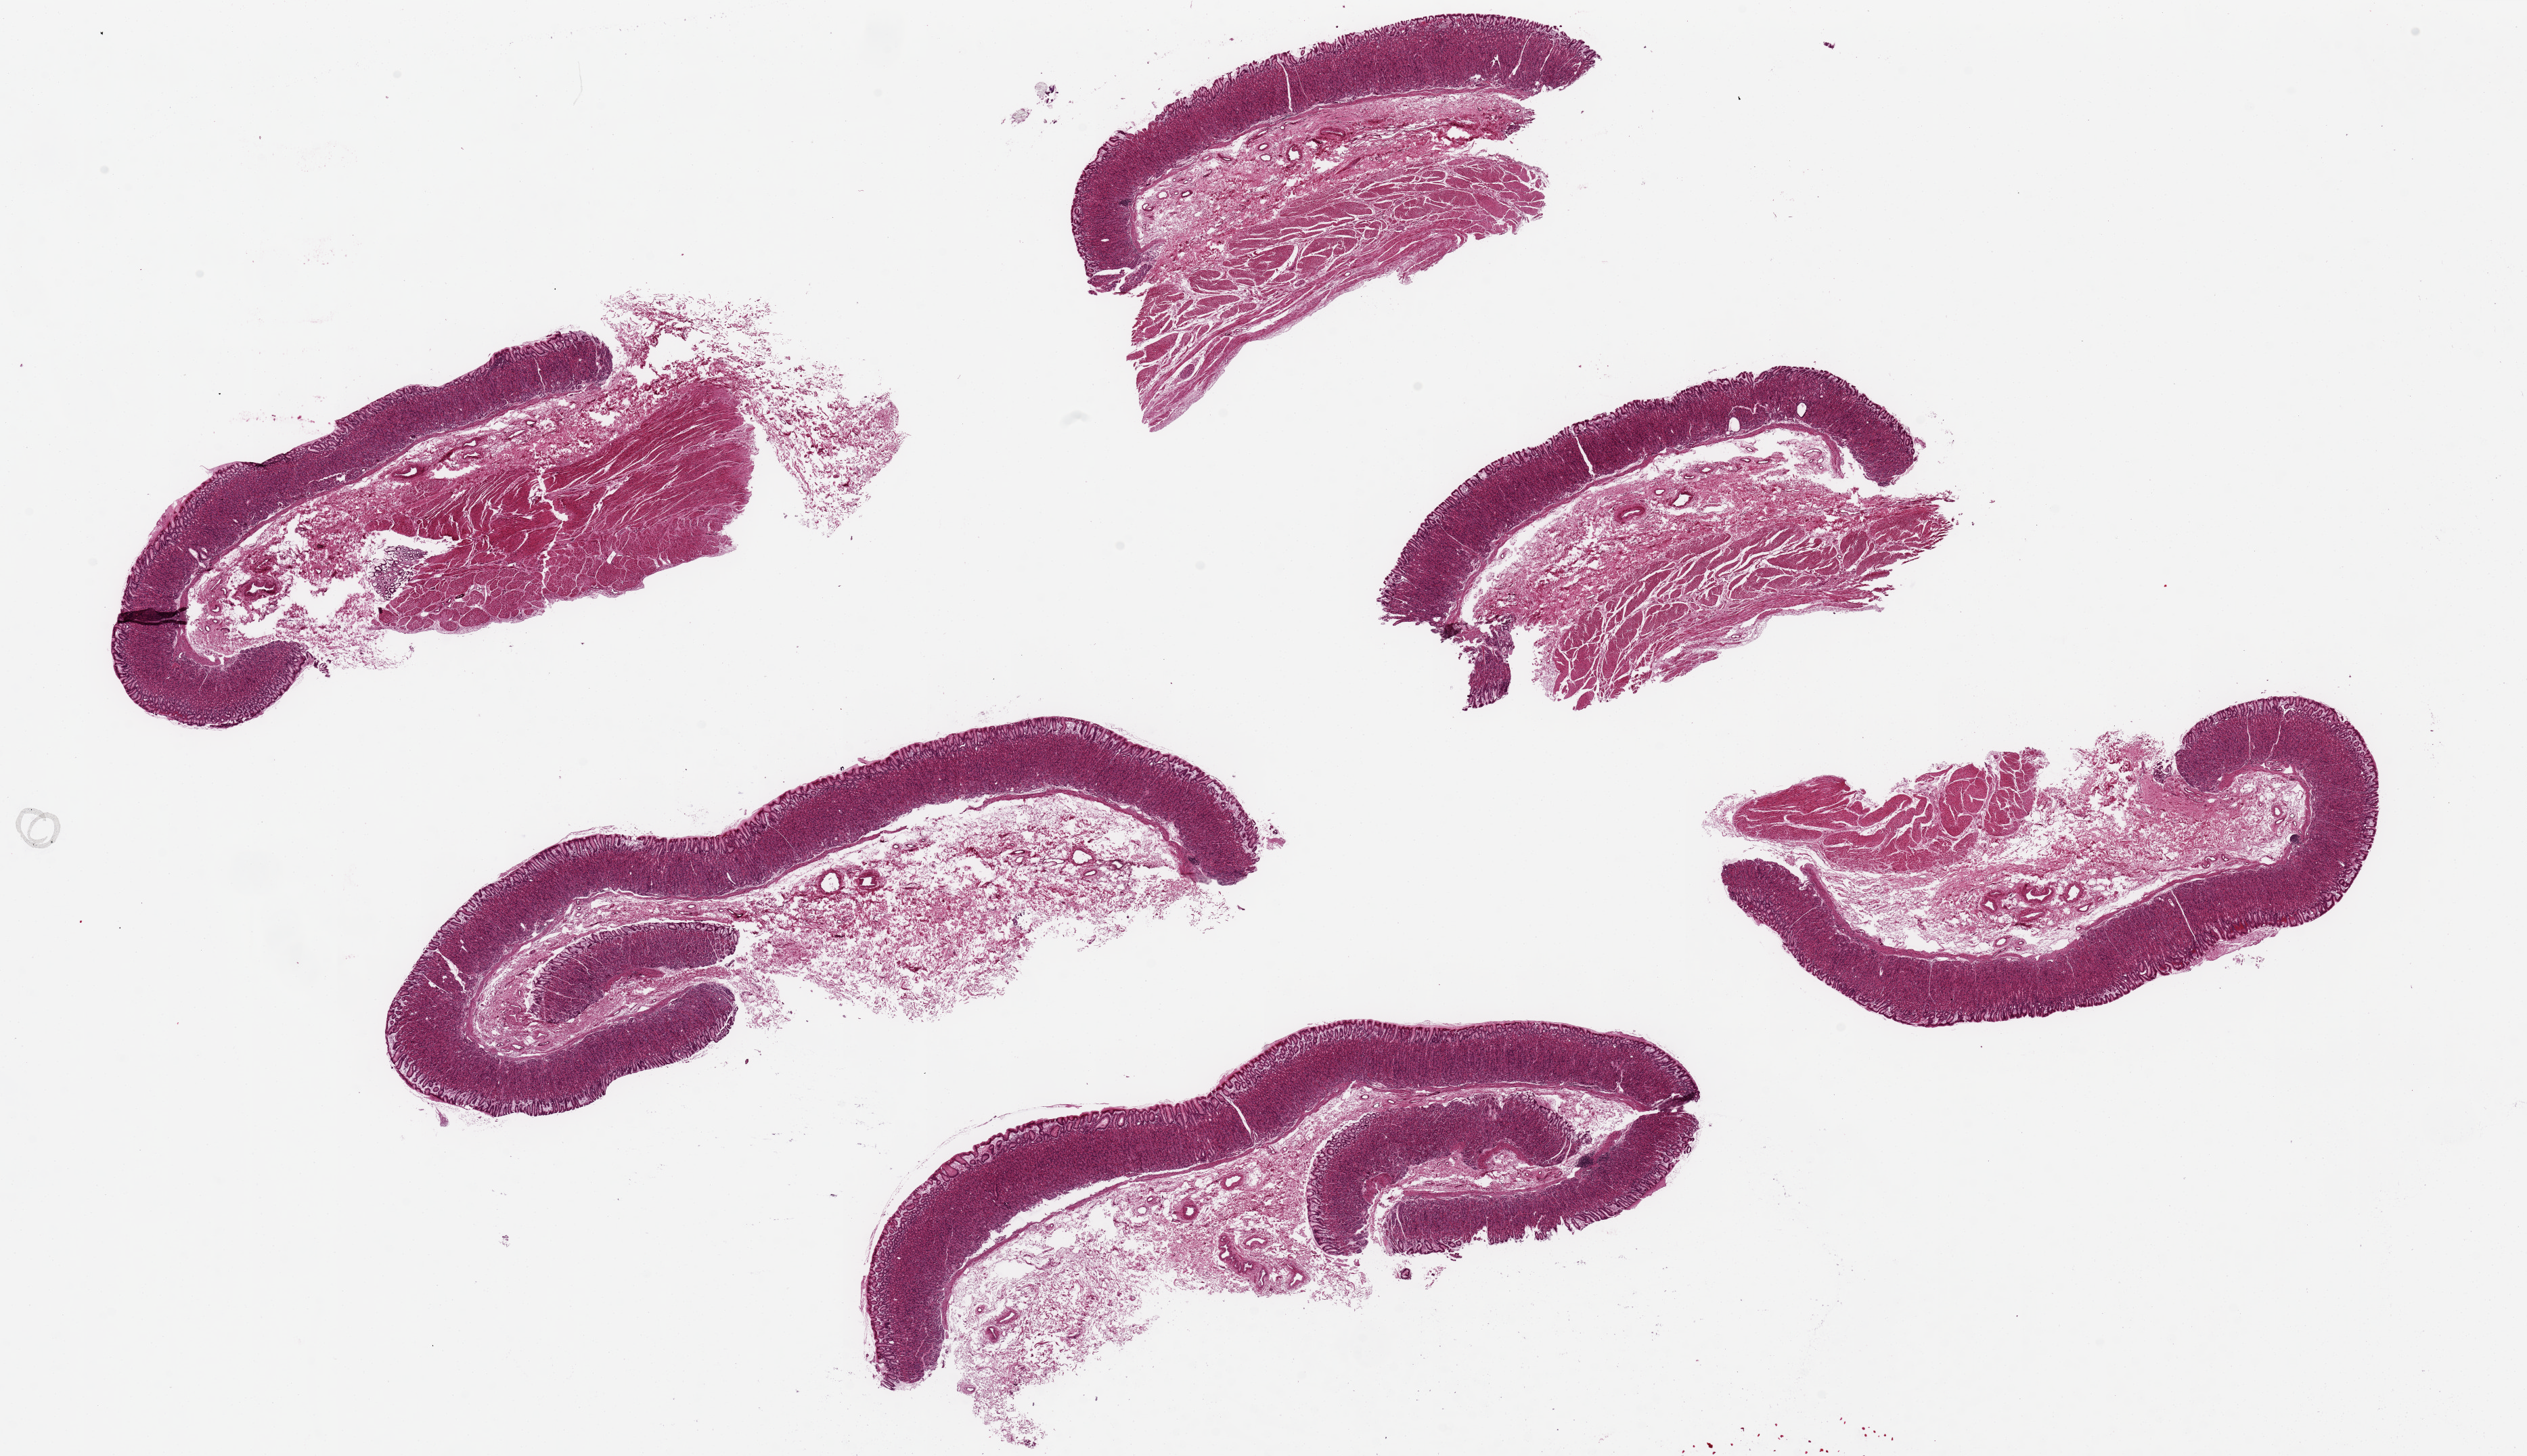
Whole-slide image, hematoxylin and eosin (H&E) stain — shown as a low-resolution overview of the whole scanned area (about 29.5 x 17.0 mm, acquisition: 20x scan), PAXgene-fixed, paraffin-embedded tissue, sampled site (target tissue): stomach, donor tissue sample. Donor sex: male.
- pathologist's review note for this sample: 6 ~8x3mm pieces; mucosa generally well preserved, ~20-25% of thickness